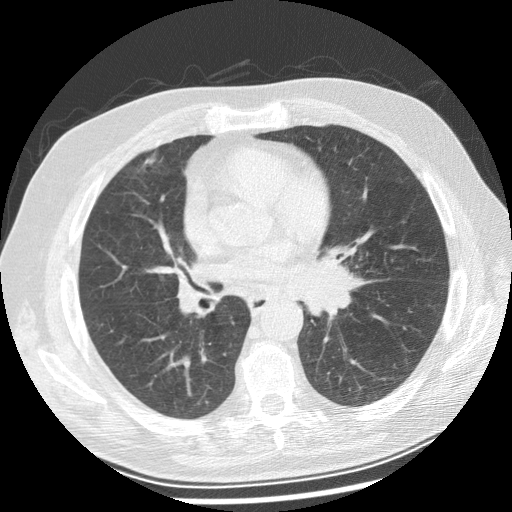
Low-dose screening chest CT, axial slice; baseline screening round; lung window (W 1500 / L -600 HU); 2.5 mm slice thickness; 512 × 512 image matrix. Male, age 70 years at enrolment. Current smoker at enrolment.
Expert-annotated lung lesion, bounding box [x1, y1, x2, y2] px = [291, 240, 375, 322]. Screening reader's record for this exam: no non-calcified nodule ≥4 mm recorded.